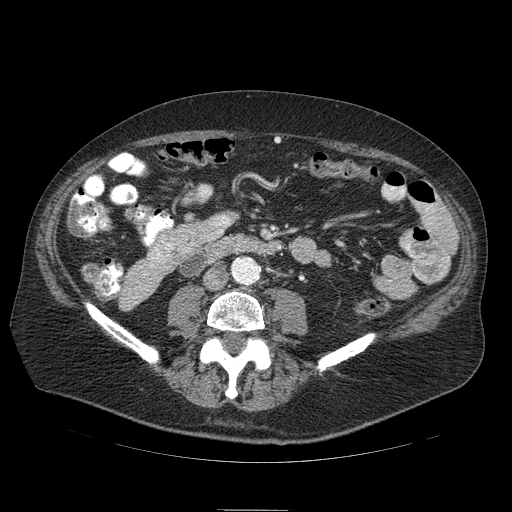
Contrast-enhanced abdominal CT (liver protocol), one axial slice. Position 9 of 103 along the scan axis. 120 kVp. Soft-tissue window (W 400 / L 40 HU). 512 × 512 image matrix. Case-level facts recorded for this patient, not image findings: diagnosis: hepatocellular carcinoma (patient treated with transarterial chemoembolisation; whether this scan precedes or follows treatment is not stated here); TNM stage (as recorded): Stage-IIIA.
Structures marked on this image (semi-automatic segmentation, software-assisted and operator-edited):
- mass: bounding box (x1, y1, x2, y2) in pixels: (149, 210, 236, 268)